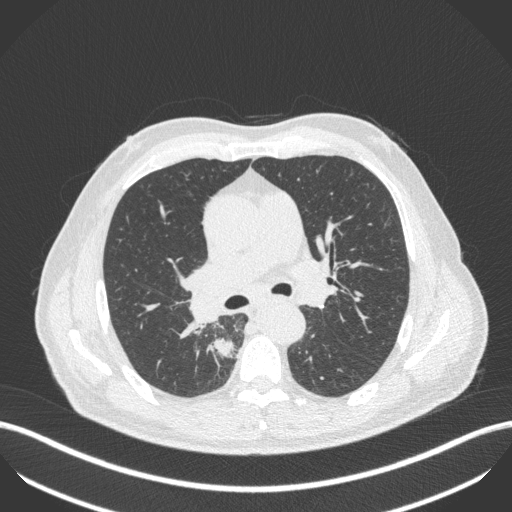
Chest CT, one axial slice; slice 283 of 451 in the series (ordered by position); 100 kVp; lung window (W 1500 / L -600 HU); 1 mm slice thickness; 512 × 512 image matrix. Patient: male, 61 years. From the clinical record (not read from this slice): clinical TNM (as recorded): T1 N0 M0.
Outlined on this slice (bounding box drawn by a radiologist):
- lung tumour (recorded histology: small cell carcinoma): bounding box [x1, y1, x2, y2] px = [207, 335, 239, 365]